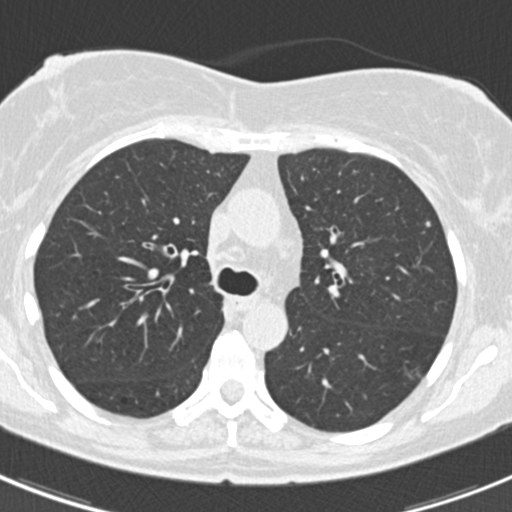
Axial slice from a low-dose chest CT screening exam; baseline screening round; lung window (W 1500 / L -600 HU); 512 × 512 image matrix, field of view 298 × 298 mm. Female participant, aged 60 years at enrolment. Current smoker at enrolment.
- Expert reader's lesion annotation, bounding box (x1, y1, x2, y2) in pixels: (417, 216, 442, 240).
- The screening reader recorded 3 non-calcified nodules or masses ≥4 mm on this exam (lingula, left lower lobe, lingula); which of them this box marks is not recorded.